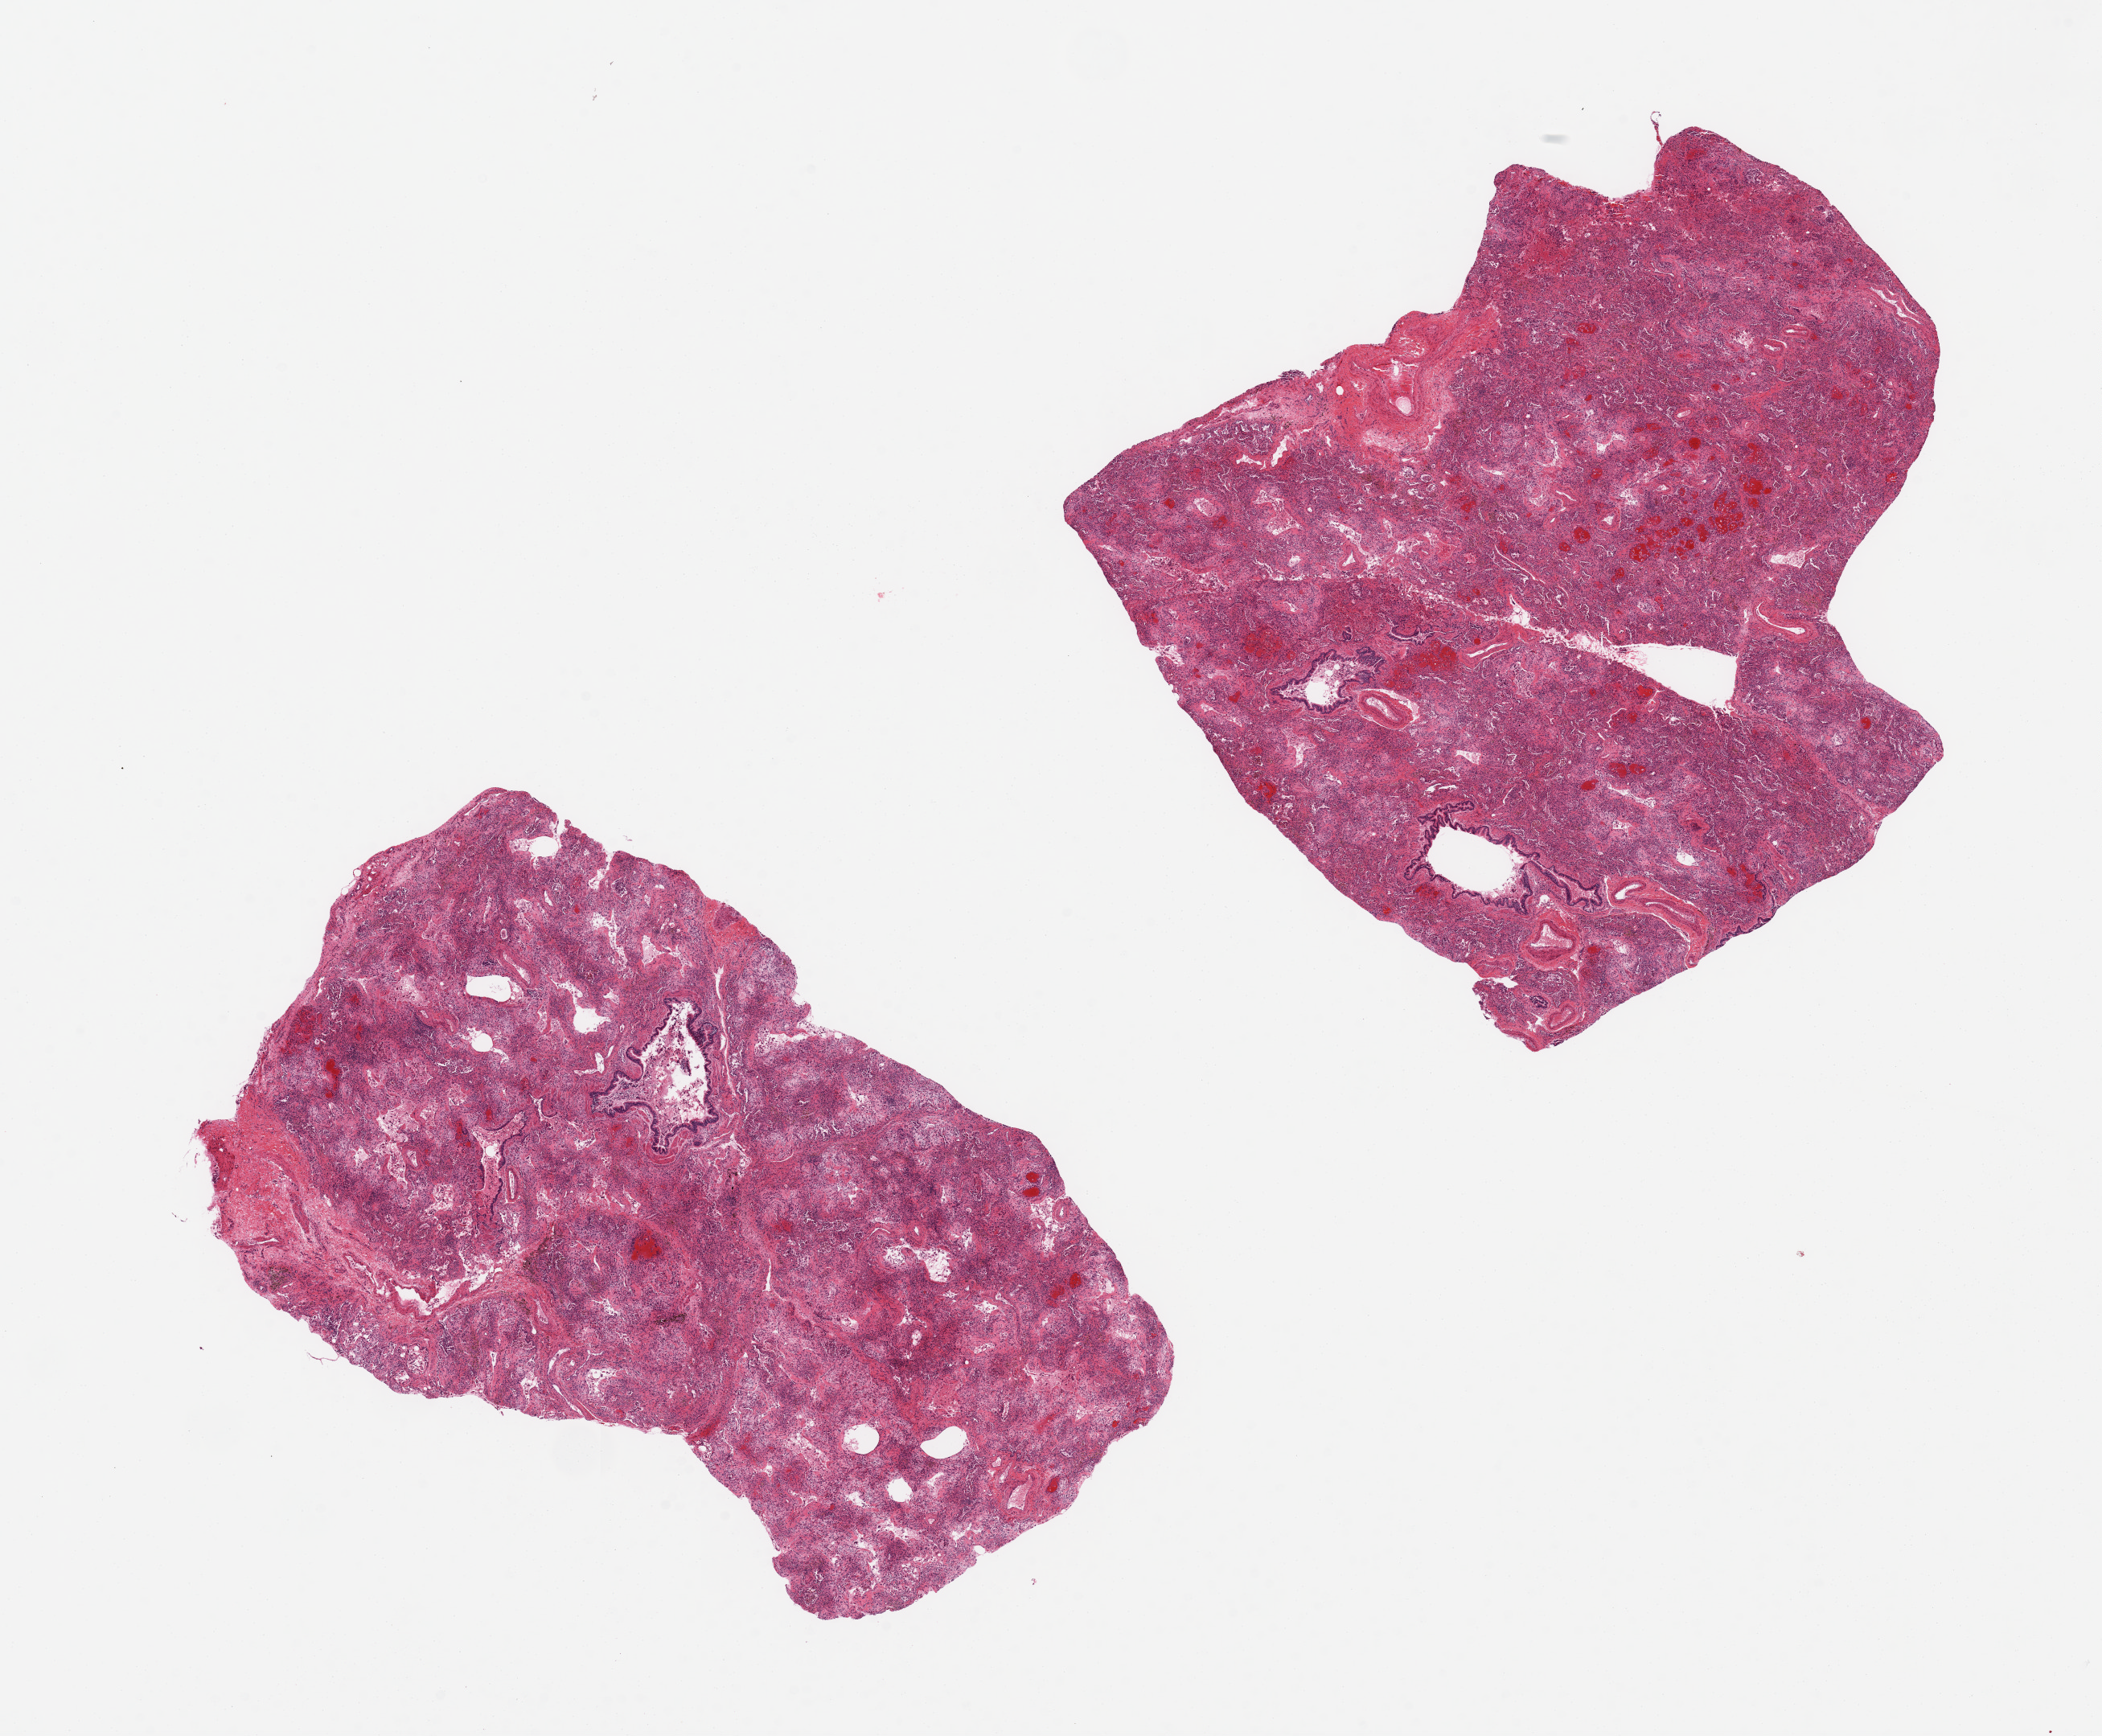
Digitized haematoxylin and eosin-stained section — shown as a low-resolution overview of the whole scanned area (about 20.7 x 17.1 mm), PAXgene-fixed, paraffin-embedded tissue, section of lung (target tissue), donor tissue sample. Female donor.
Review note (as recorded): 2 pieces, severe chronic fibrosing chronic and focally acute pneumonitis, features of DAD.